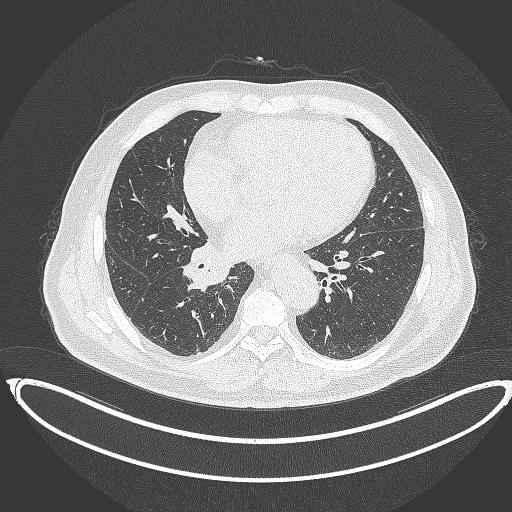
Chest CT, one axial slice. Slice 177 of 387 in the series (ordered by position). Reconstruction kernel B70f. Lung window (W 1500 / L -600 HU). 512 × 512 image matrix, field of view 448 × 448 mm. Male patient, age 61 years. From the clinical record (not read from this slice): clinical TNM (as recorded): T1b N1 M0.
Structures marked on this image (bounding box drawn by a radiologist):
- lung tumour (recorded histology: squamous cell carcinoma): bounding box <178,234,236,292> (left, top, right, bottom; pixels)